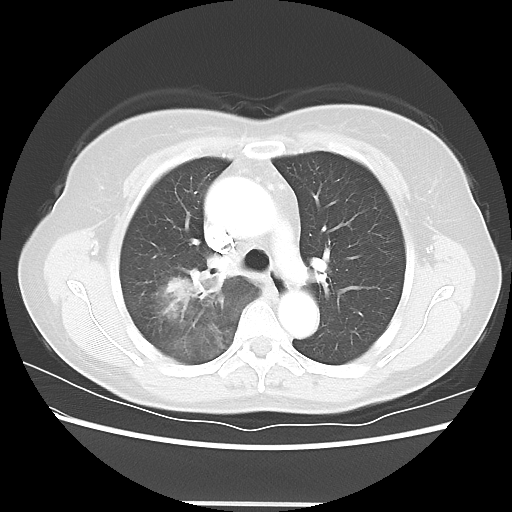
Chest CT, one axial slice; position 40 of 56 along the scan axis; reconstruction kernel LUNG; 120 kVp; lung window (W 1500 / L -600 HU); 5 mm slice thickness; 512 × 512 image matrix, field of view 360 × 360 mm. Female patient, age 55 years. From the clinical record (not read from this slice): clinical TNM (as recorded): T2 N1 M0.
Outlined on this slice (bounding box drawn by a radiologist):
- lung tumour (recorded histology: adenocarcinoma): bounding box [x1, y1, x2, y2] px = [137, 251, 225, 324]